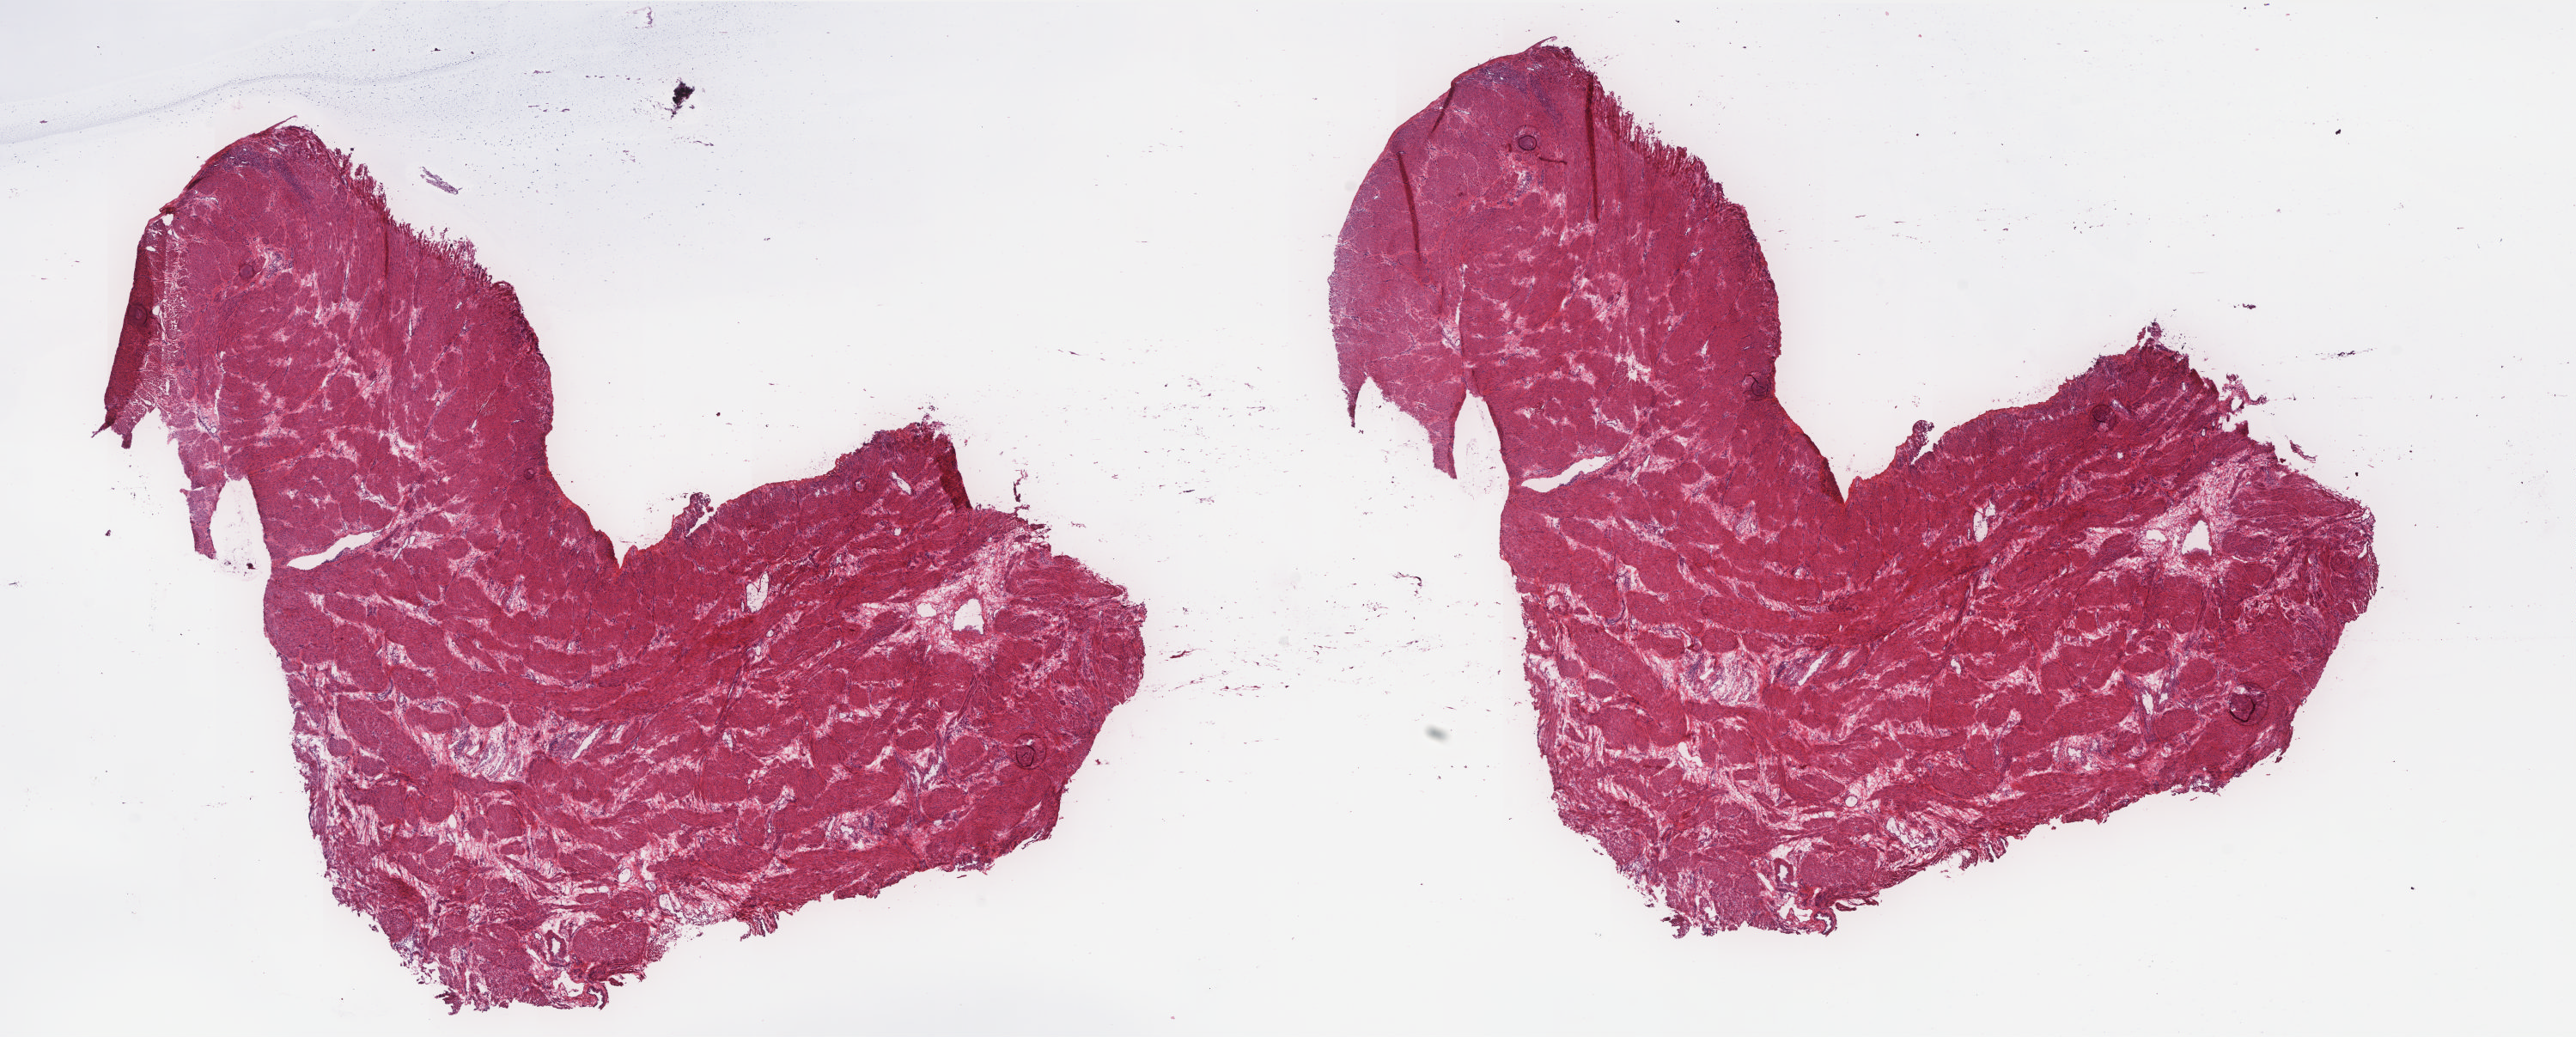
H&E whole-slide image, a low-resolution overview of the entire scanned area, about 24.0 x 9.6 mm (from a 20x scan), frozen section from the top of the tissue portion, uterus, solid tissue normal (non-tumour tissue) sample. Patient: female, age at initial diagnosis 60 years. Slide review estimates, as recorded: tumour cells 0%, normal cells 100%. Infiltration values recorded for this section: lymphocyte infiltration 5%, monocyte infiltration 0%, neutrophil infiltration 0%.
This section: solid tissue normal (non-tumour) sample from the same patient. Patient diagnosis: Endometrioid adenocarcinoma, NOS (endometrium).